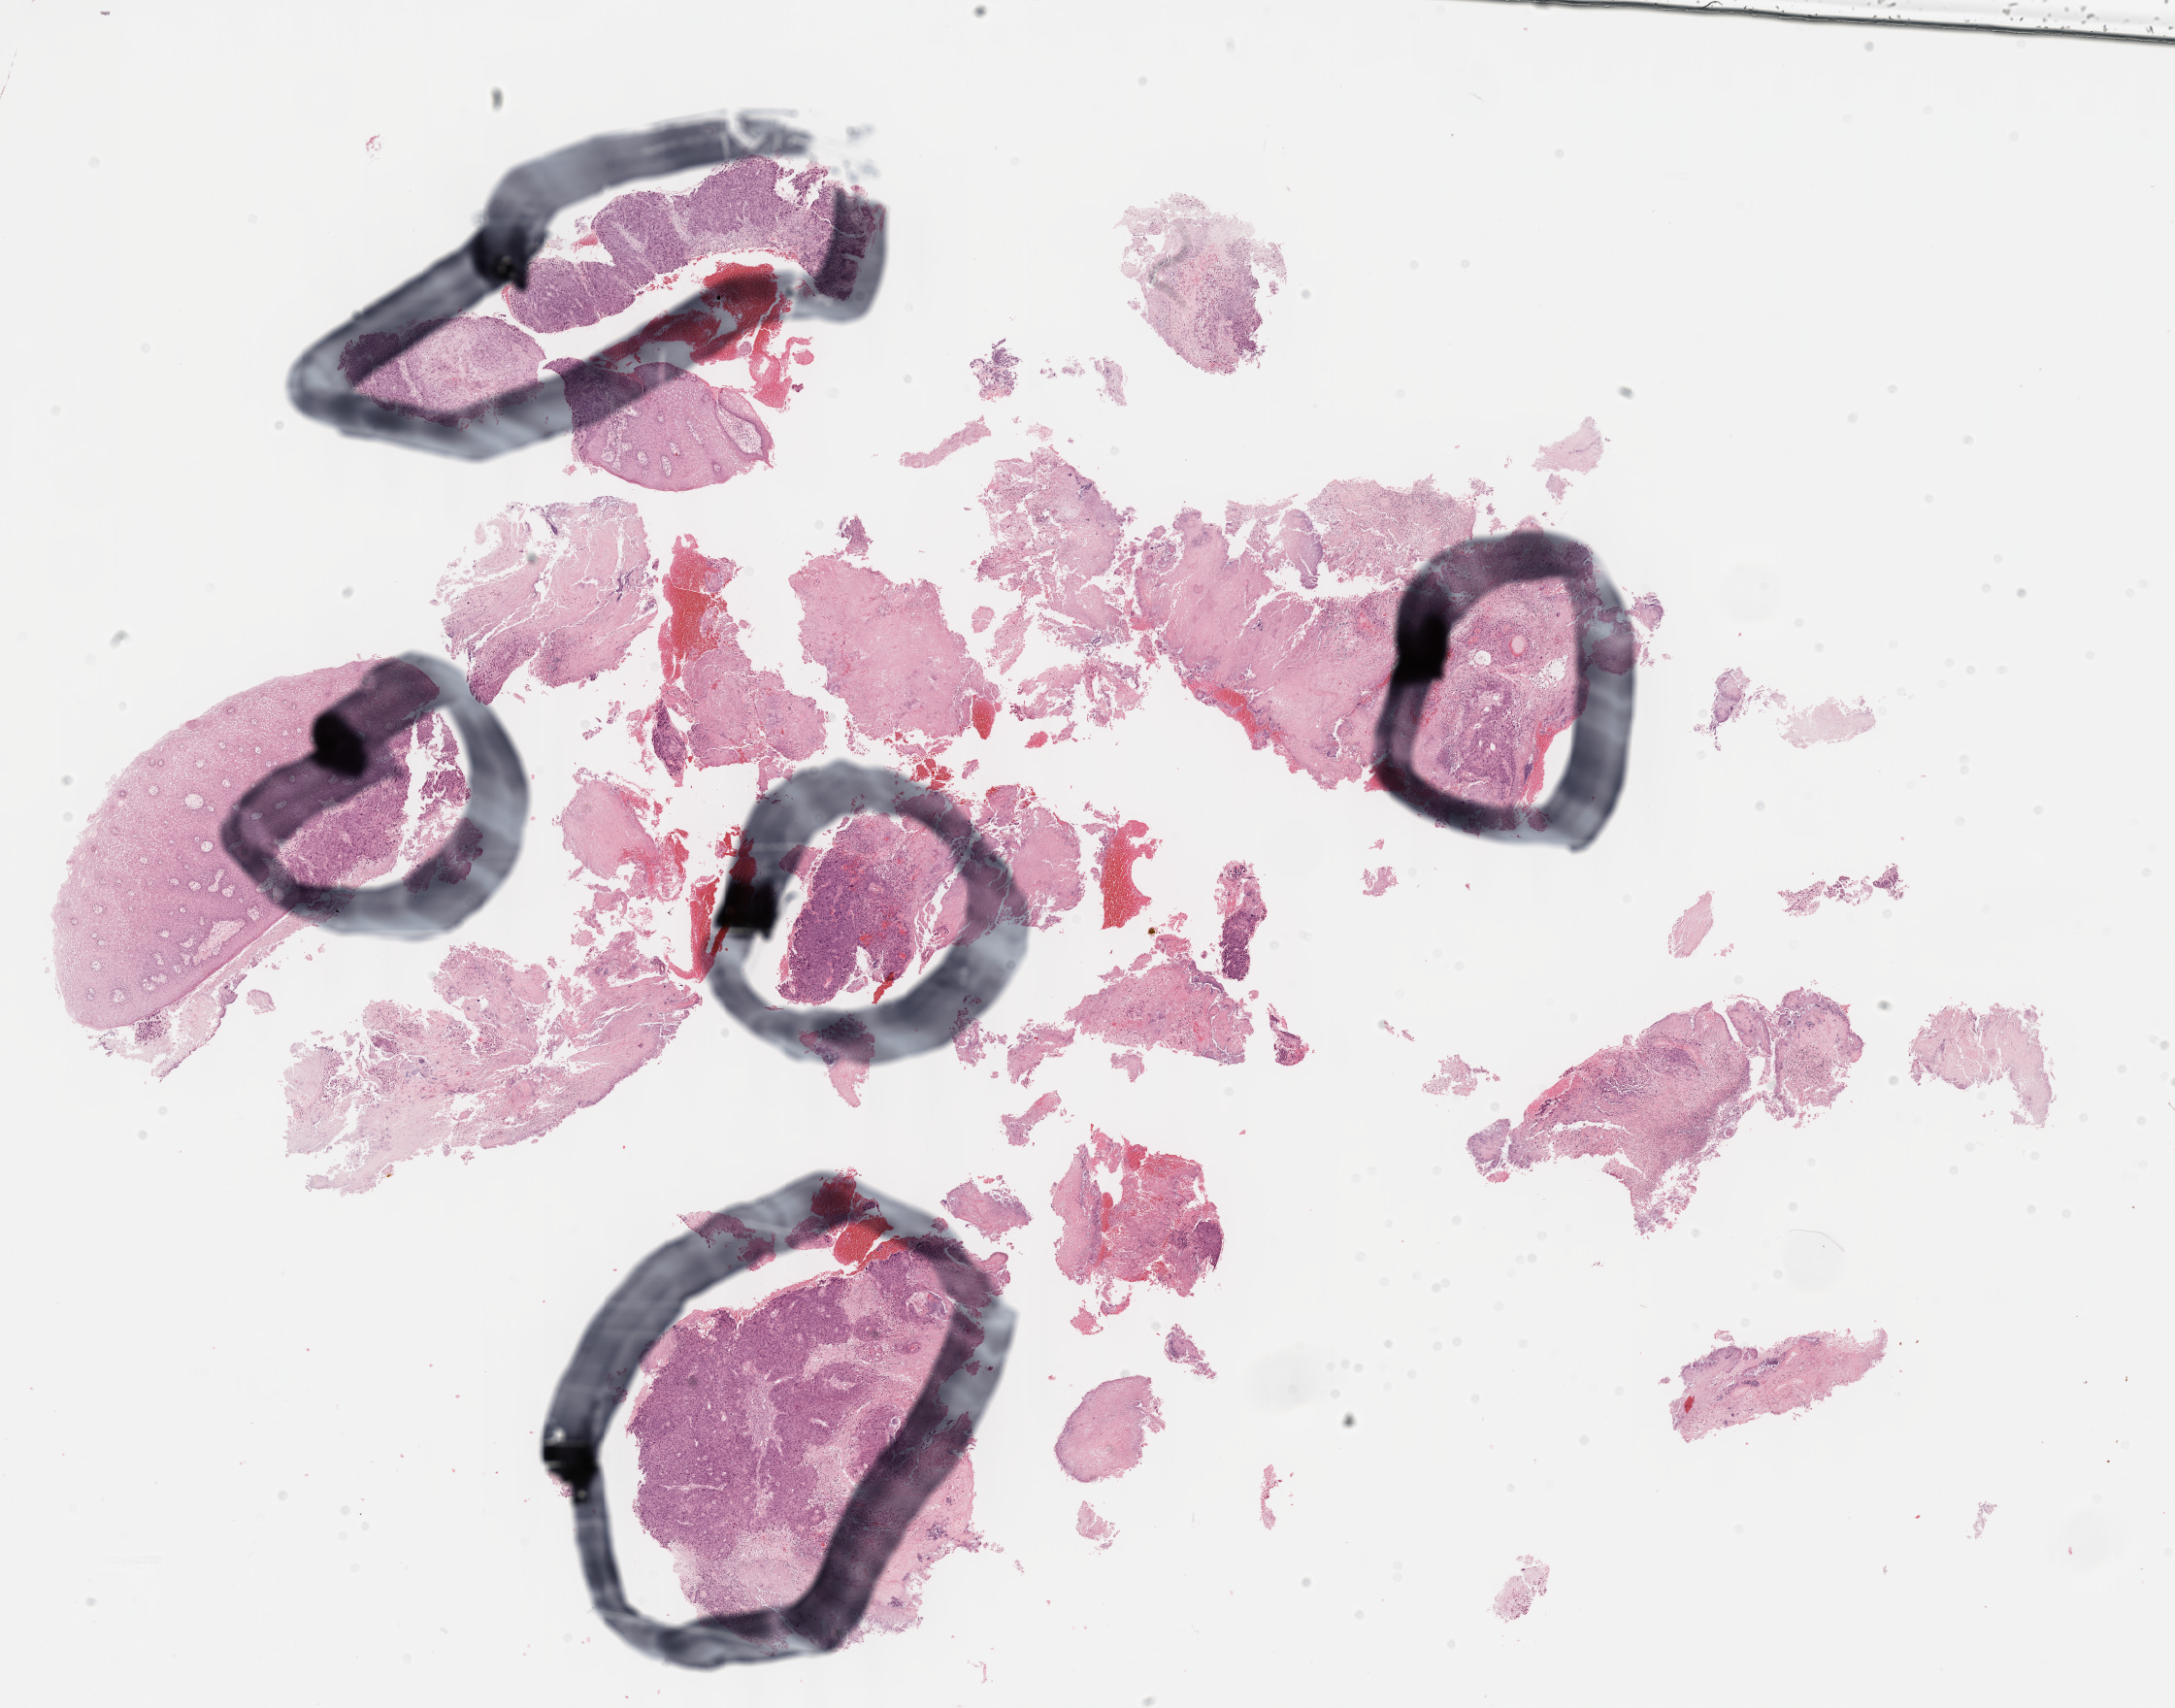
H&E-stained whole-slide image, whole scanned area (about 18.1 x 14.2 mm) shown as a low-resolution overview, FFPE section, head and neck, primary tumour sample. Patient: male, age at initial diagnosis 65 years. Histologic grade: G3 (poorly differentiated).
• diagnosis: Squamous cell carcinoma, NOS (overlapping lesion of lip, oral cavity and pharynx)